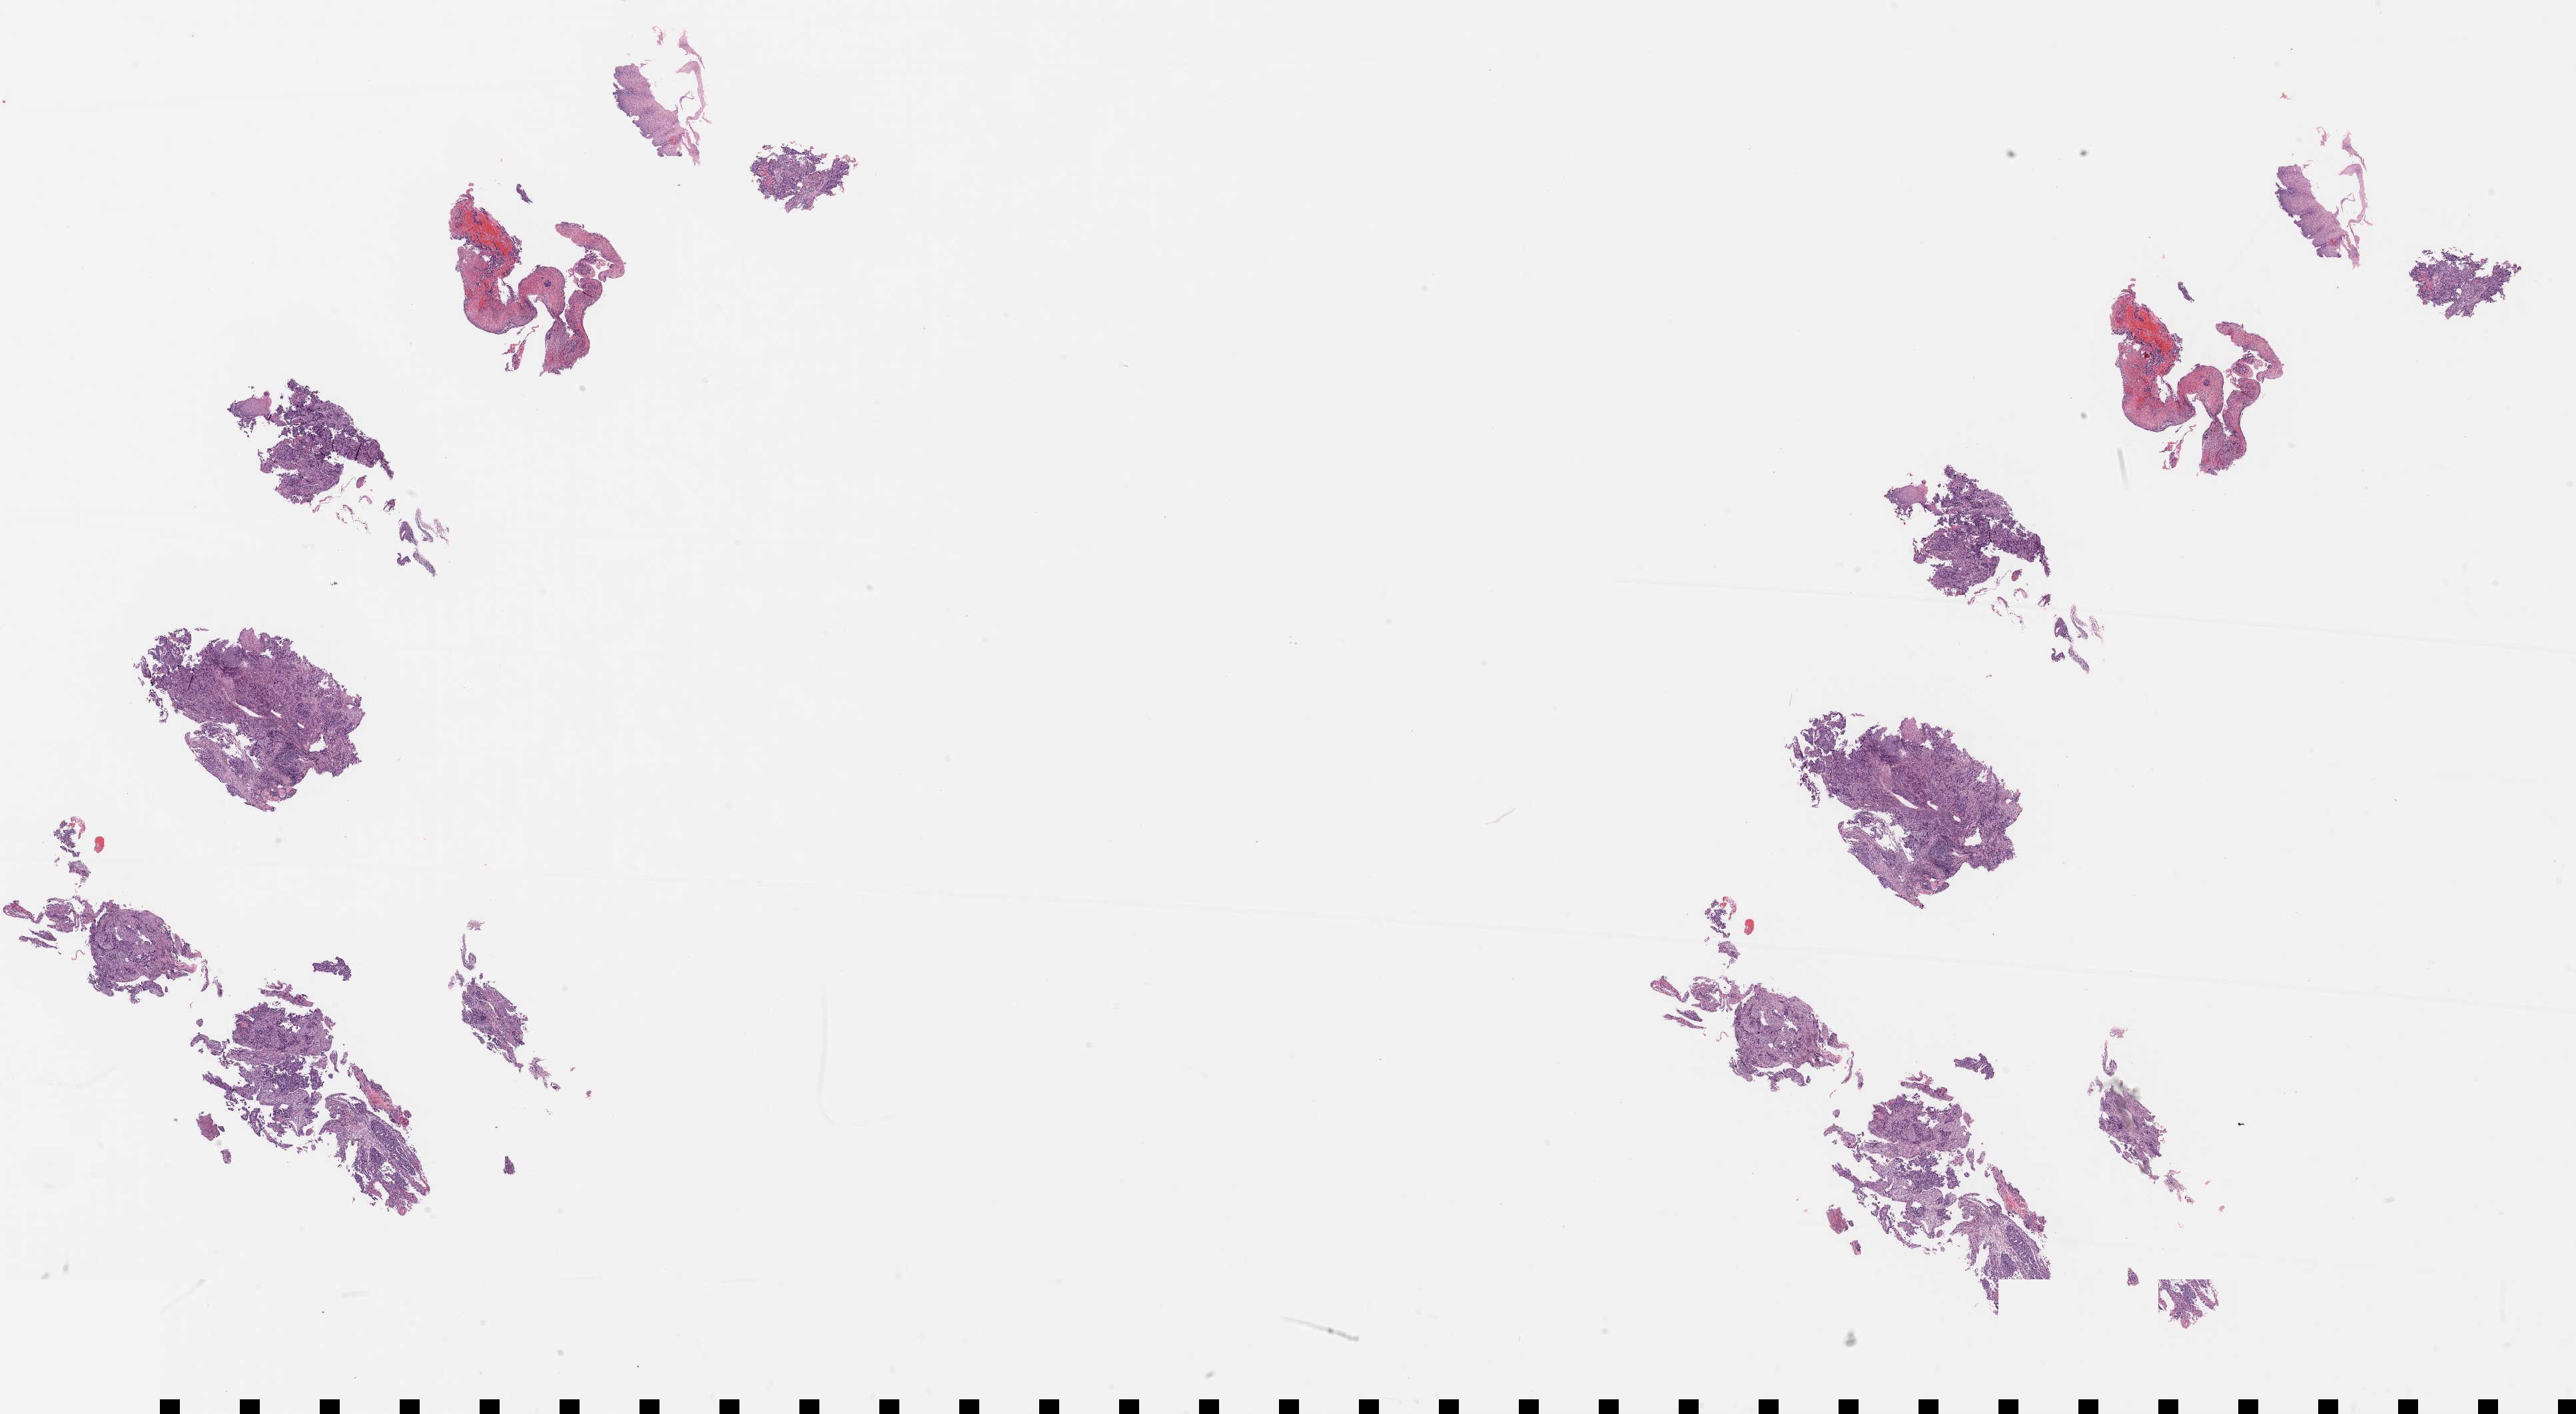
H&E whole-slide image, low-resolution overview of the scanned area, about 30.4 x 16.7 mm (from a 40x scan); FFPE section; sample: primary tumour, esophagus. Male patient; age at initial diagnosis 68 years. Histologic grade: G3 (poorly differentiated). Composition of this section per pathologist review: tumour cells 50%, tumour nuclei 60%, normal cells 10%, stromal cells 40%, necrosis 0%. Inflammatory infiltration, as recorded: lymphocyte infiltration 0%, monocyte infiltration 0%, neutrophil infiltration 0%.
Histologic diagnosis: Adenocarcinoma, NOS.